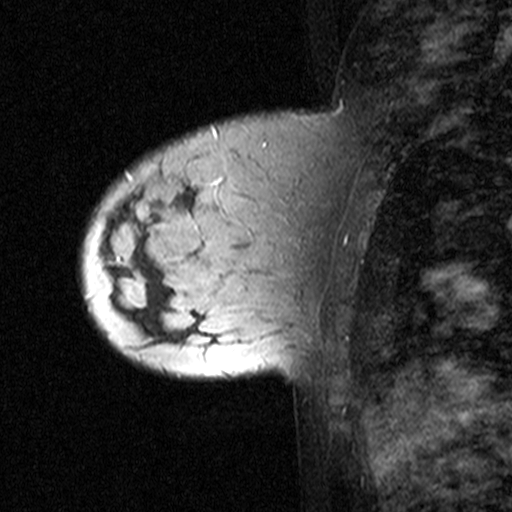
Breast MRI (dynamic contrast-enhanced), one sagittal slice. Slice 11 of 44 in the series (ordered by position). Dynamic contrast-enhanced study with each time point stored as its own series, time point 2 of 3 at this slice position (early post-contrast, ordered by acquisition time). 1.5 T. TE 4.5 ms, TR 11 ms. 3 mm slice thickness. 512 × 512 image matrix. Female patient, age 27 years. From the clinical record (not read from this slice): setting: breast cancer imaged before/during neoadjuvant chemotherapy; receptor status: HR-positive, HER2-negative.
Annotated regions visible in this slice (semi-automatic segmentation, software-assisted and operator-edited):
- analysis volume of interest (the breast-tissue region the enhancement analysis was run in; not a lesion): bounding box (x1, y1, x2, y2) in pixels: (81, 162, 163, 271)
- tumour enhancement mask (voxels above the 90 % enhancement threshold inside the analysis volume of interest): (126, 173, 132, 178)